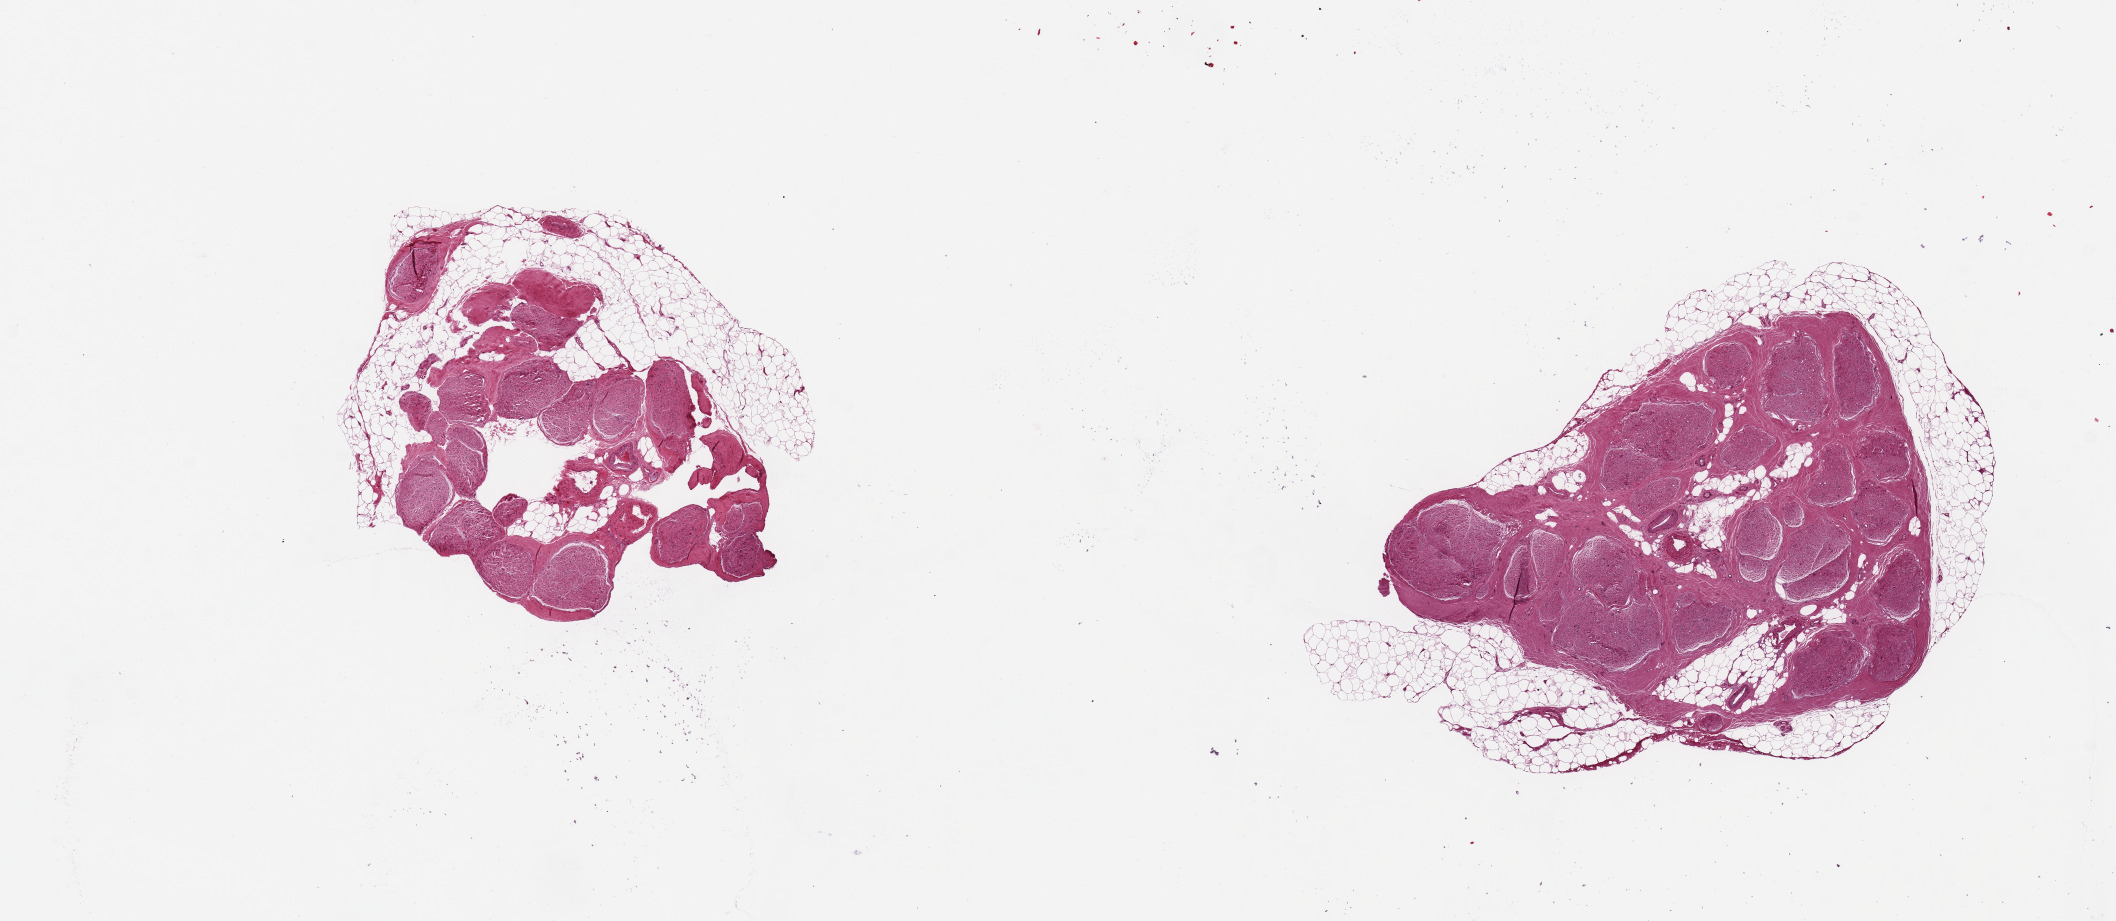
Digitized hematoxylin and eosin (H&E)-stained section, whole scanned area (about 16.7 x 7.3 mm, from a 20x scan) shown as a low-resolution overview. PAXgene-fixed, paraffin-embedded tissue. Sampled site (target tissue): tibial nerve. Donor tissue sample. Donor sex: male.
• reviewer comment on this tissue sample: 2 pieces, 4x3 & 5x4mm; ~40% adipose